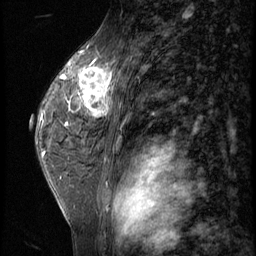
Breast MRI (dynamic contrast-enhanced), one sagittal slice; position 39 of 62 along the scan axis; 3 images stored at this slice position (order not interpretable as contrast timing); 1.5 T; TE 4.2 ms, TR 9 ms; 2.5 mm slice thickness; 256 × 256 image matrix. Patient: female, 44 years. From the clinical record (not read from this slice): setting: breast cancer imaged before/during neoadjuvant chemotherapy; receptor status: triple-negative.
Structures marked on this image (semi-automatic segmentation, software-assisted and operator-edited):
- analysis volume of interest (the breast-tissue region the enhancement analysis was run in; not a lesion): bounding box <70,64,116,125> (left, top, right, bottom; pixels)
- tumour enhancement mask (voxels above the 140 % enhancement threshold inside the analysis volume of interest): <71,64,116,119>